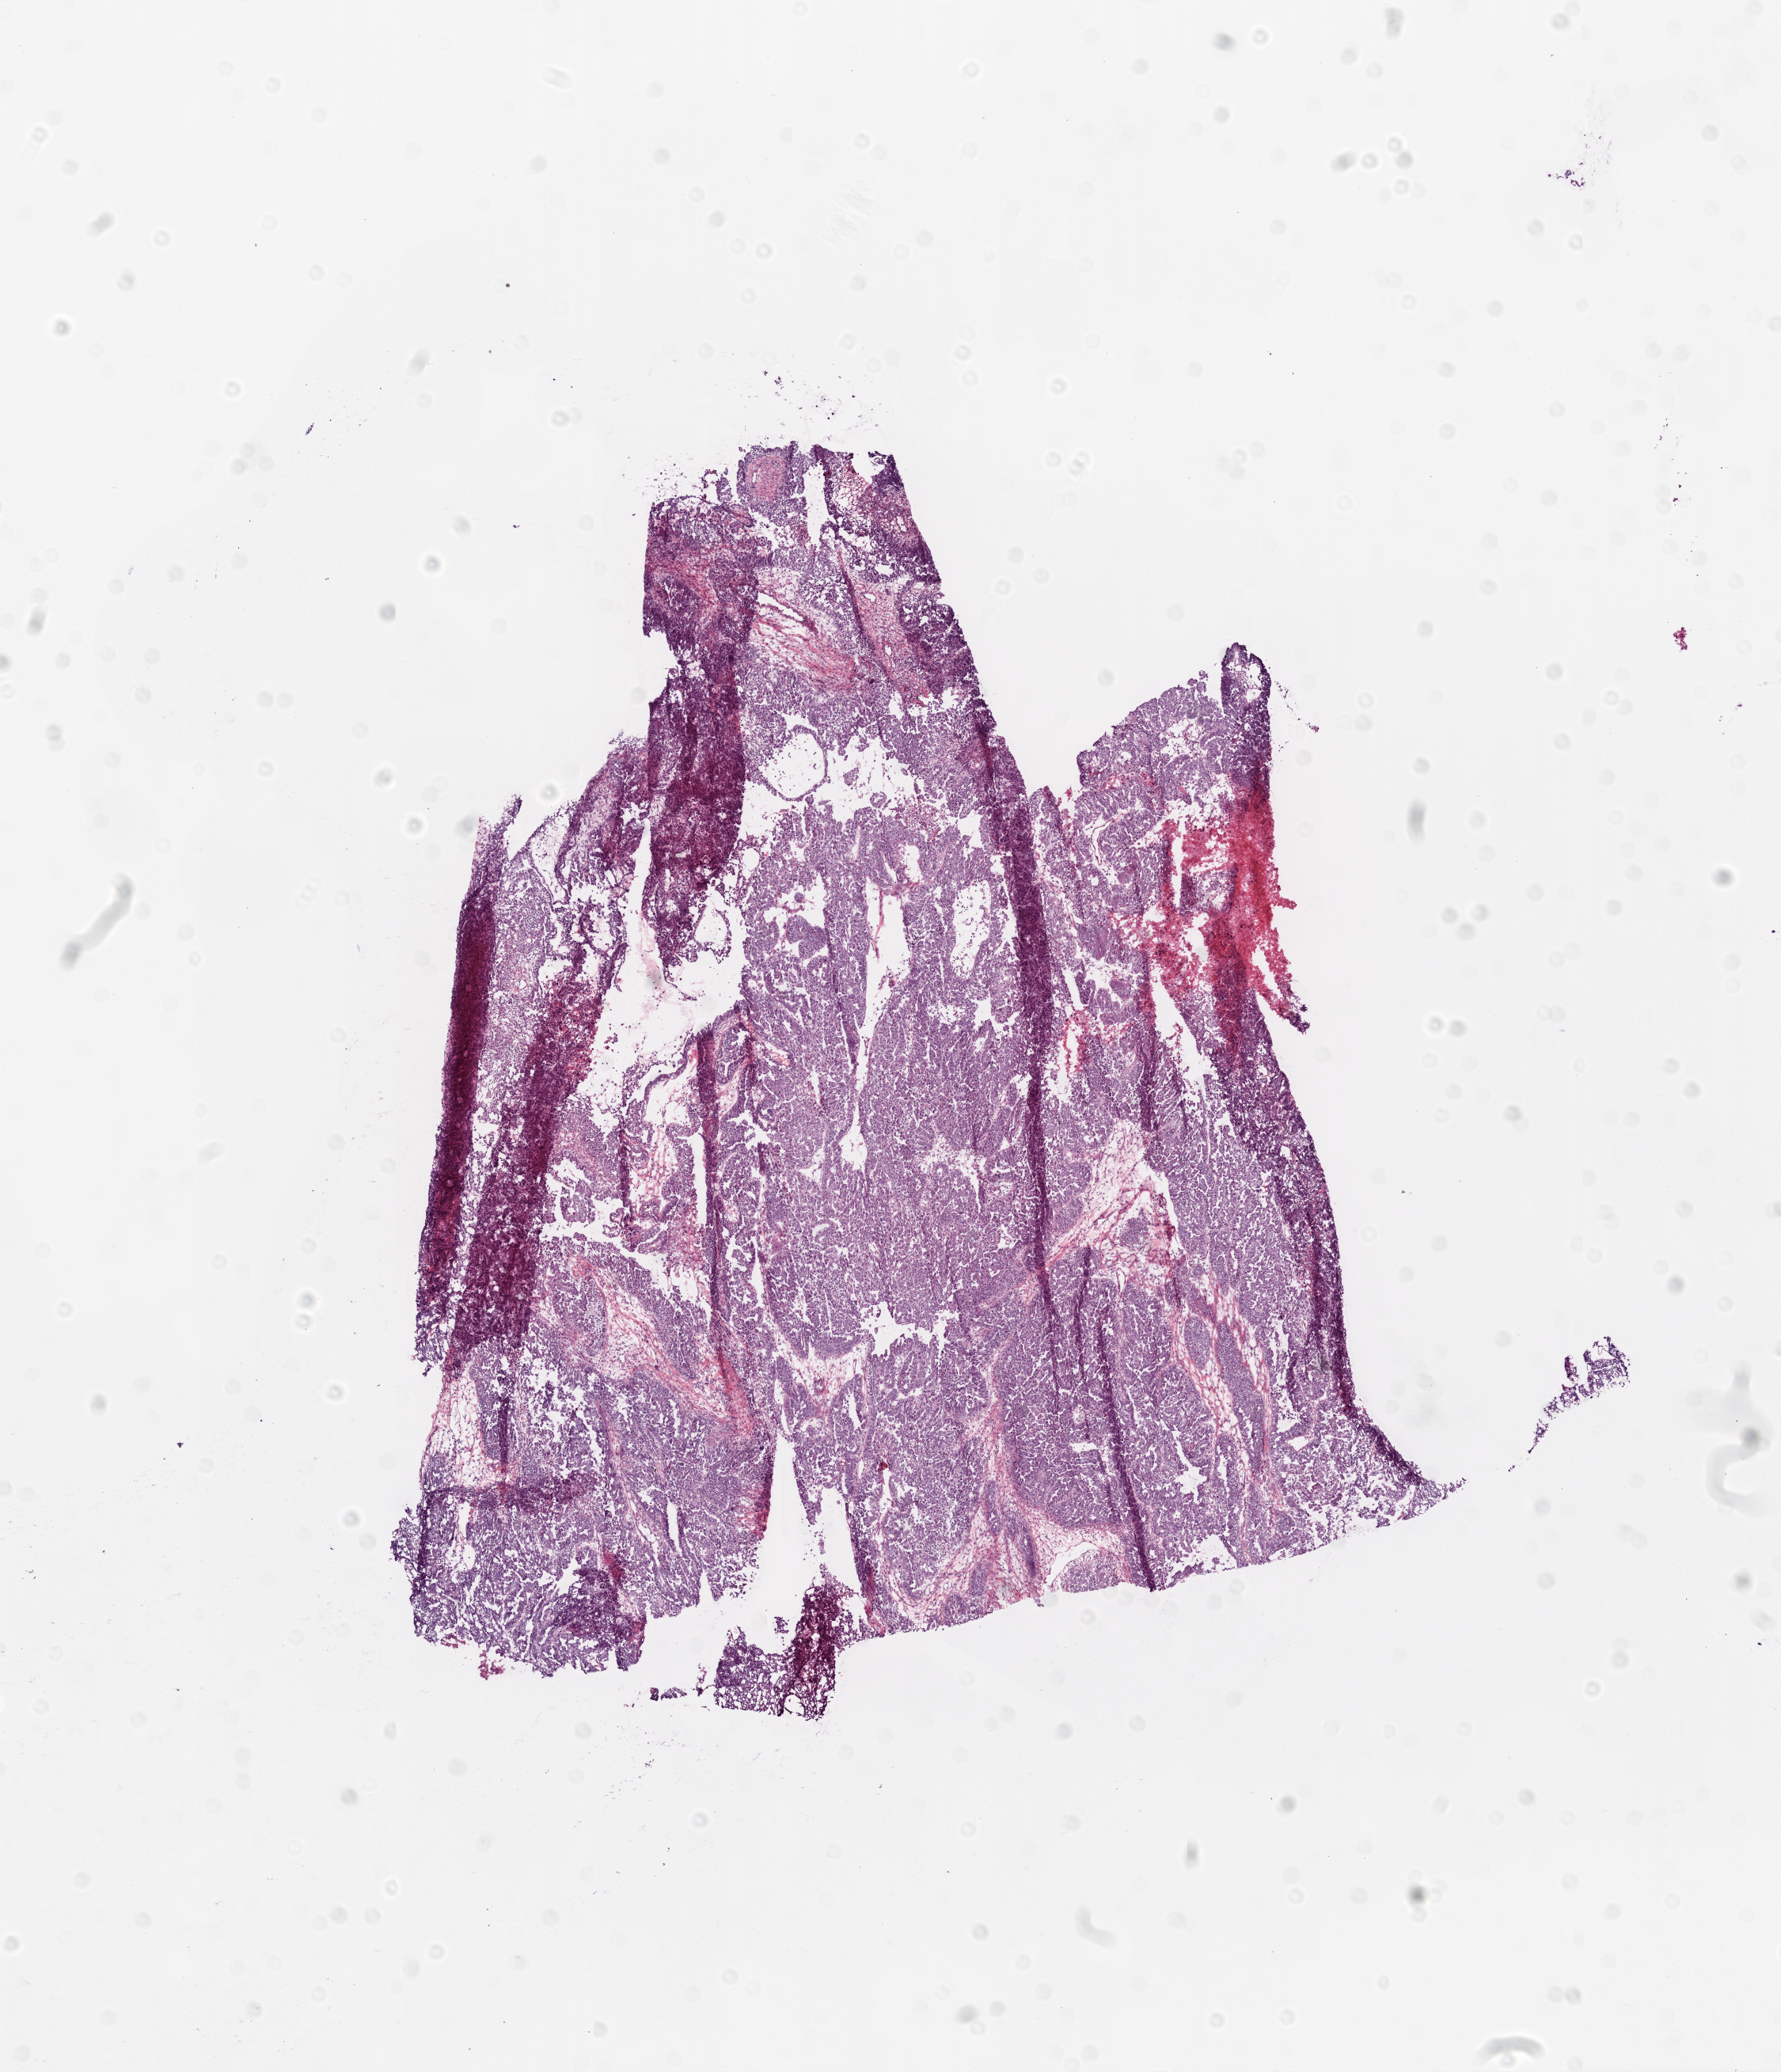
H&E-stained whole-slide image, whole scanned area (about 9.0 x 10.5 mm) shown as a low-resolution overview. Frozen section from the bottom of the tissue portion. Sample: primary tumour, ovary. Patient: female, age at initial diagnosis 62 years. Histologic grade: G3 (poorly differentiated). Composition of this section per pathologist review: tumour cells 60%, tumour nuclei 80%, normal cells 0%, stromal cells 40%, necrosis 0%.
* diagnosis: Serous cystadenocarcinoma, NOS
* FIGO stage: IC